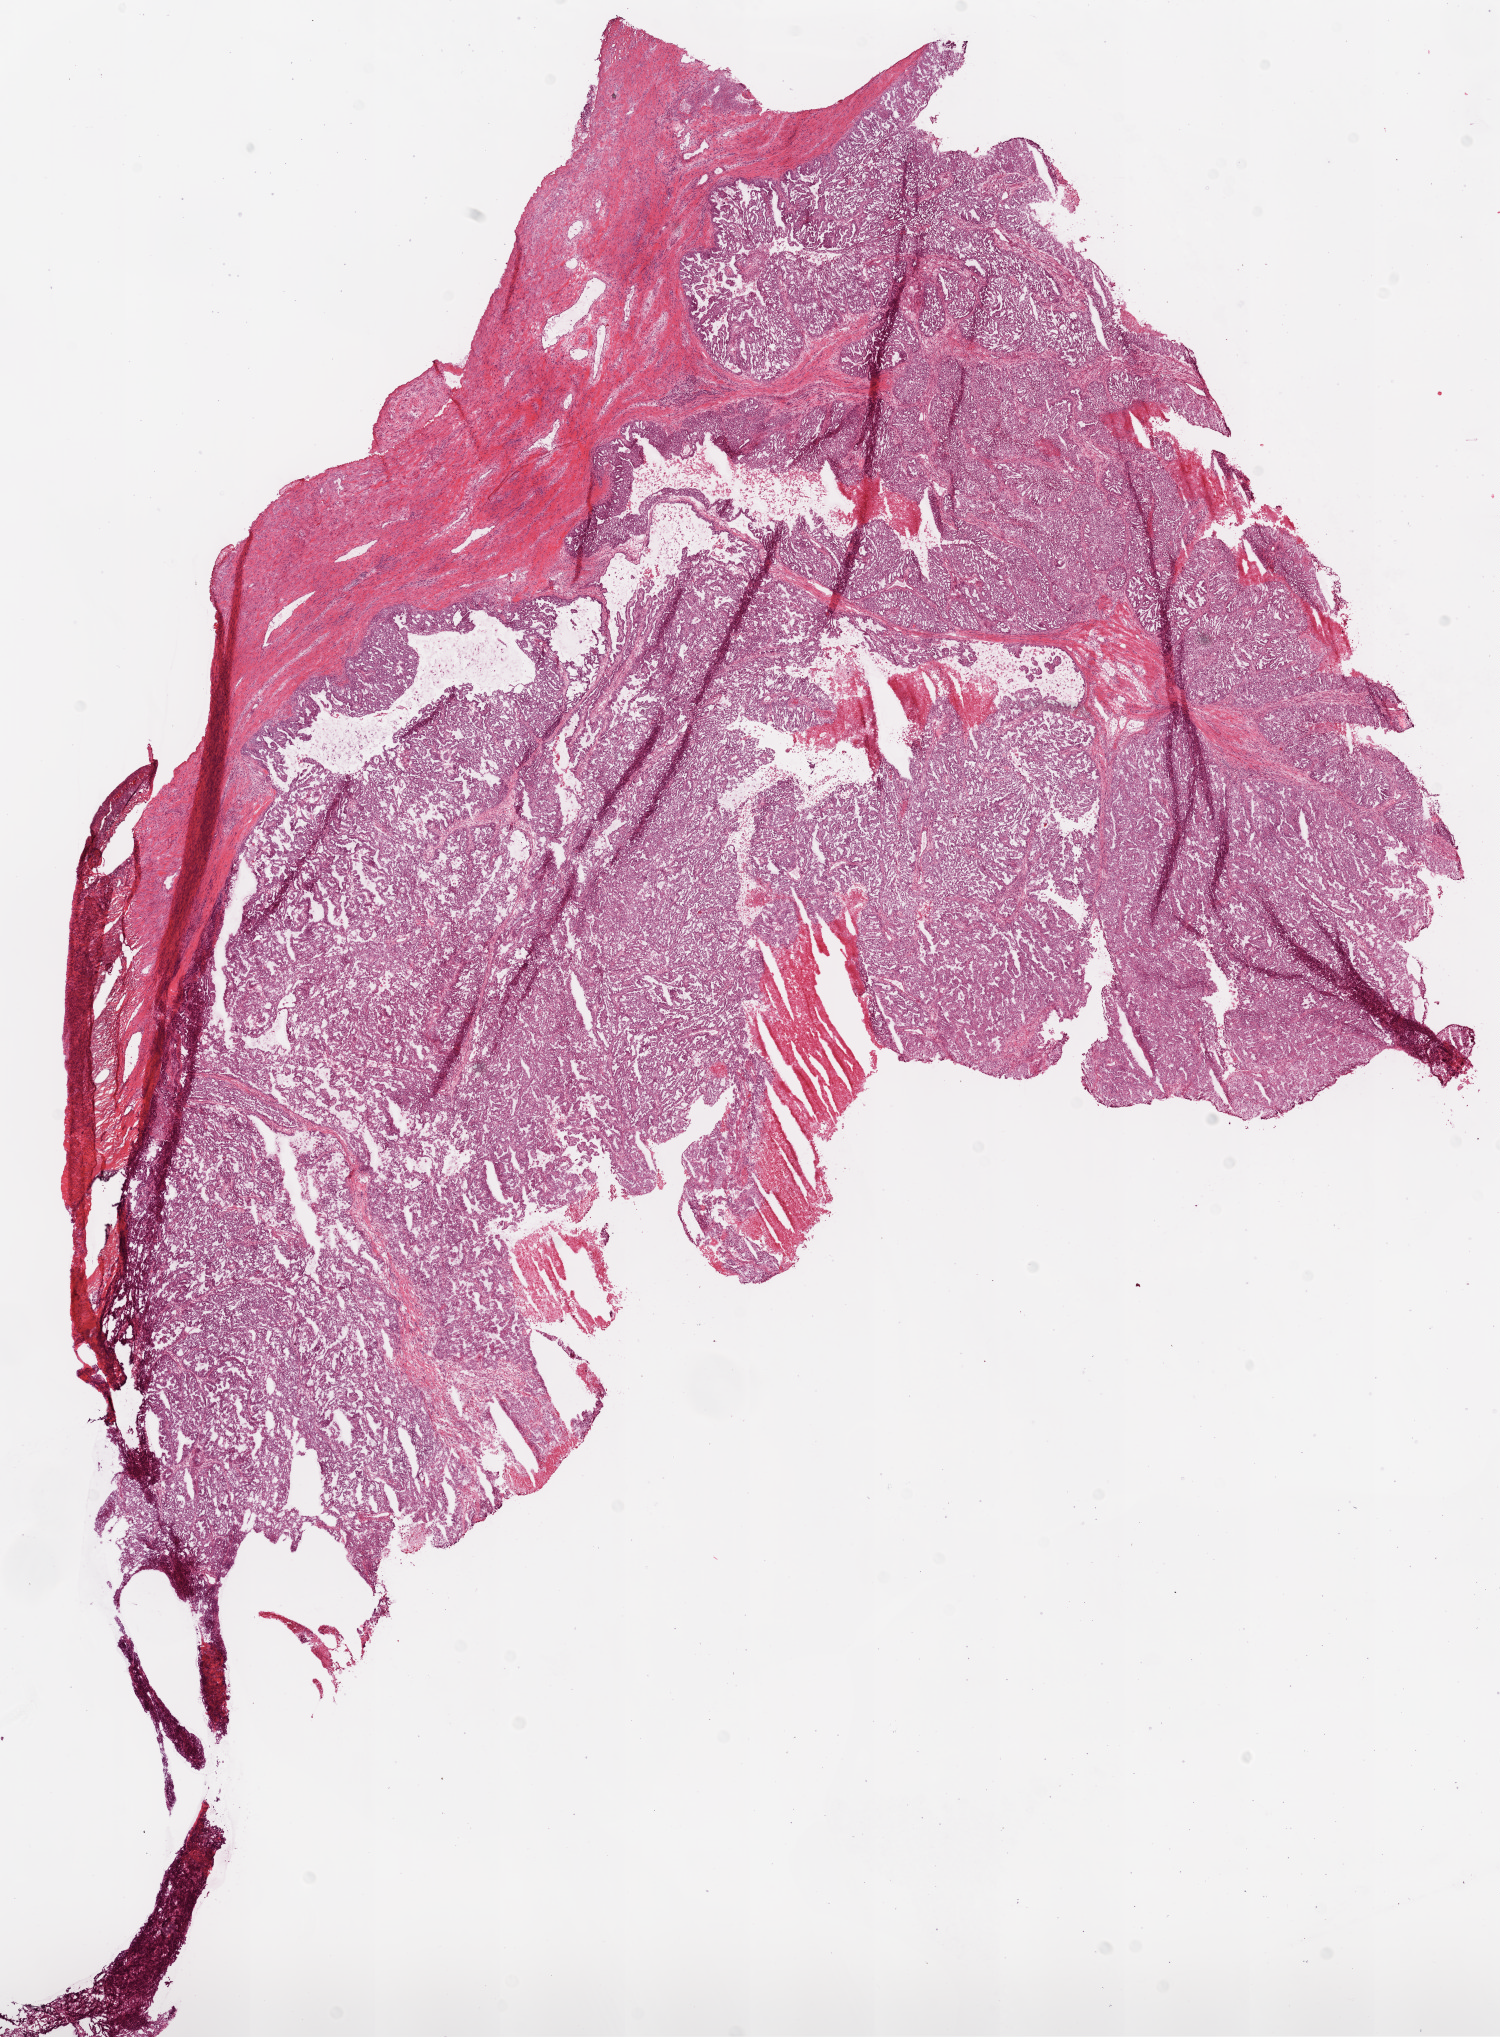
Digitized H&E tissue section (whole slide) — a low-resolution overview of the entire scanned area, about 12.0 x 16.3 mm, frozen section from the bottom of the tissue portion, sample: primary tumour, ovary. Female, age 59 years at initial diagnosis. Histologic grade: G3 (poorly differentiated). Pathologist review of this section (percent, as recorded): tumour cells 90%, tumour nuclei 90%, normal cells 0%, stromal cells 10%, necrosis 0%. Infiltration values recorded for this section: lymphocyte infiltration 0%, monocyte infiltration 0%, neutrophil infiltration 0%.
• FIGO stage: IIC
• diagnosis: Serous cystadenocarcinoma, NOS